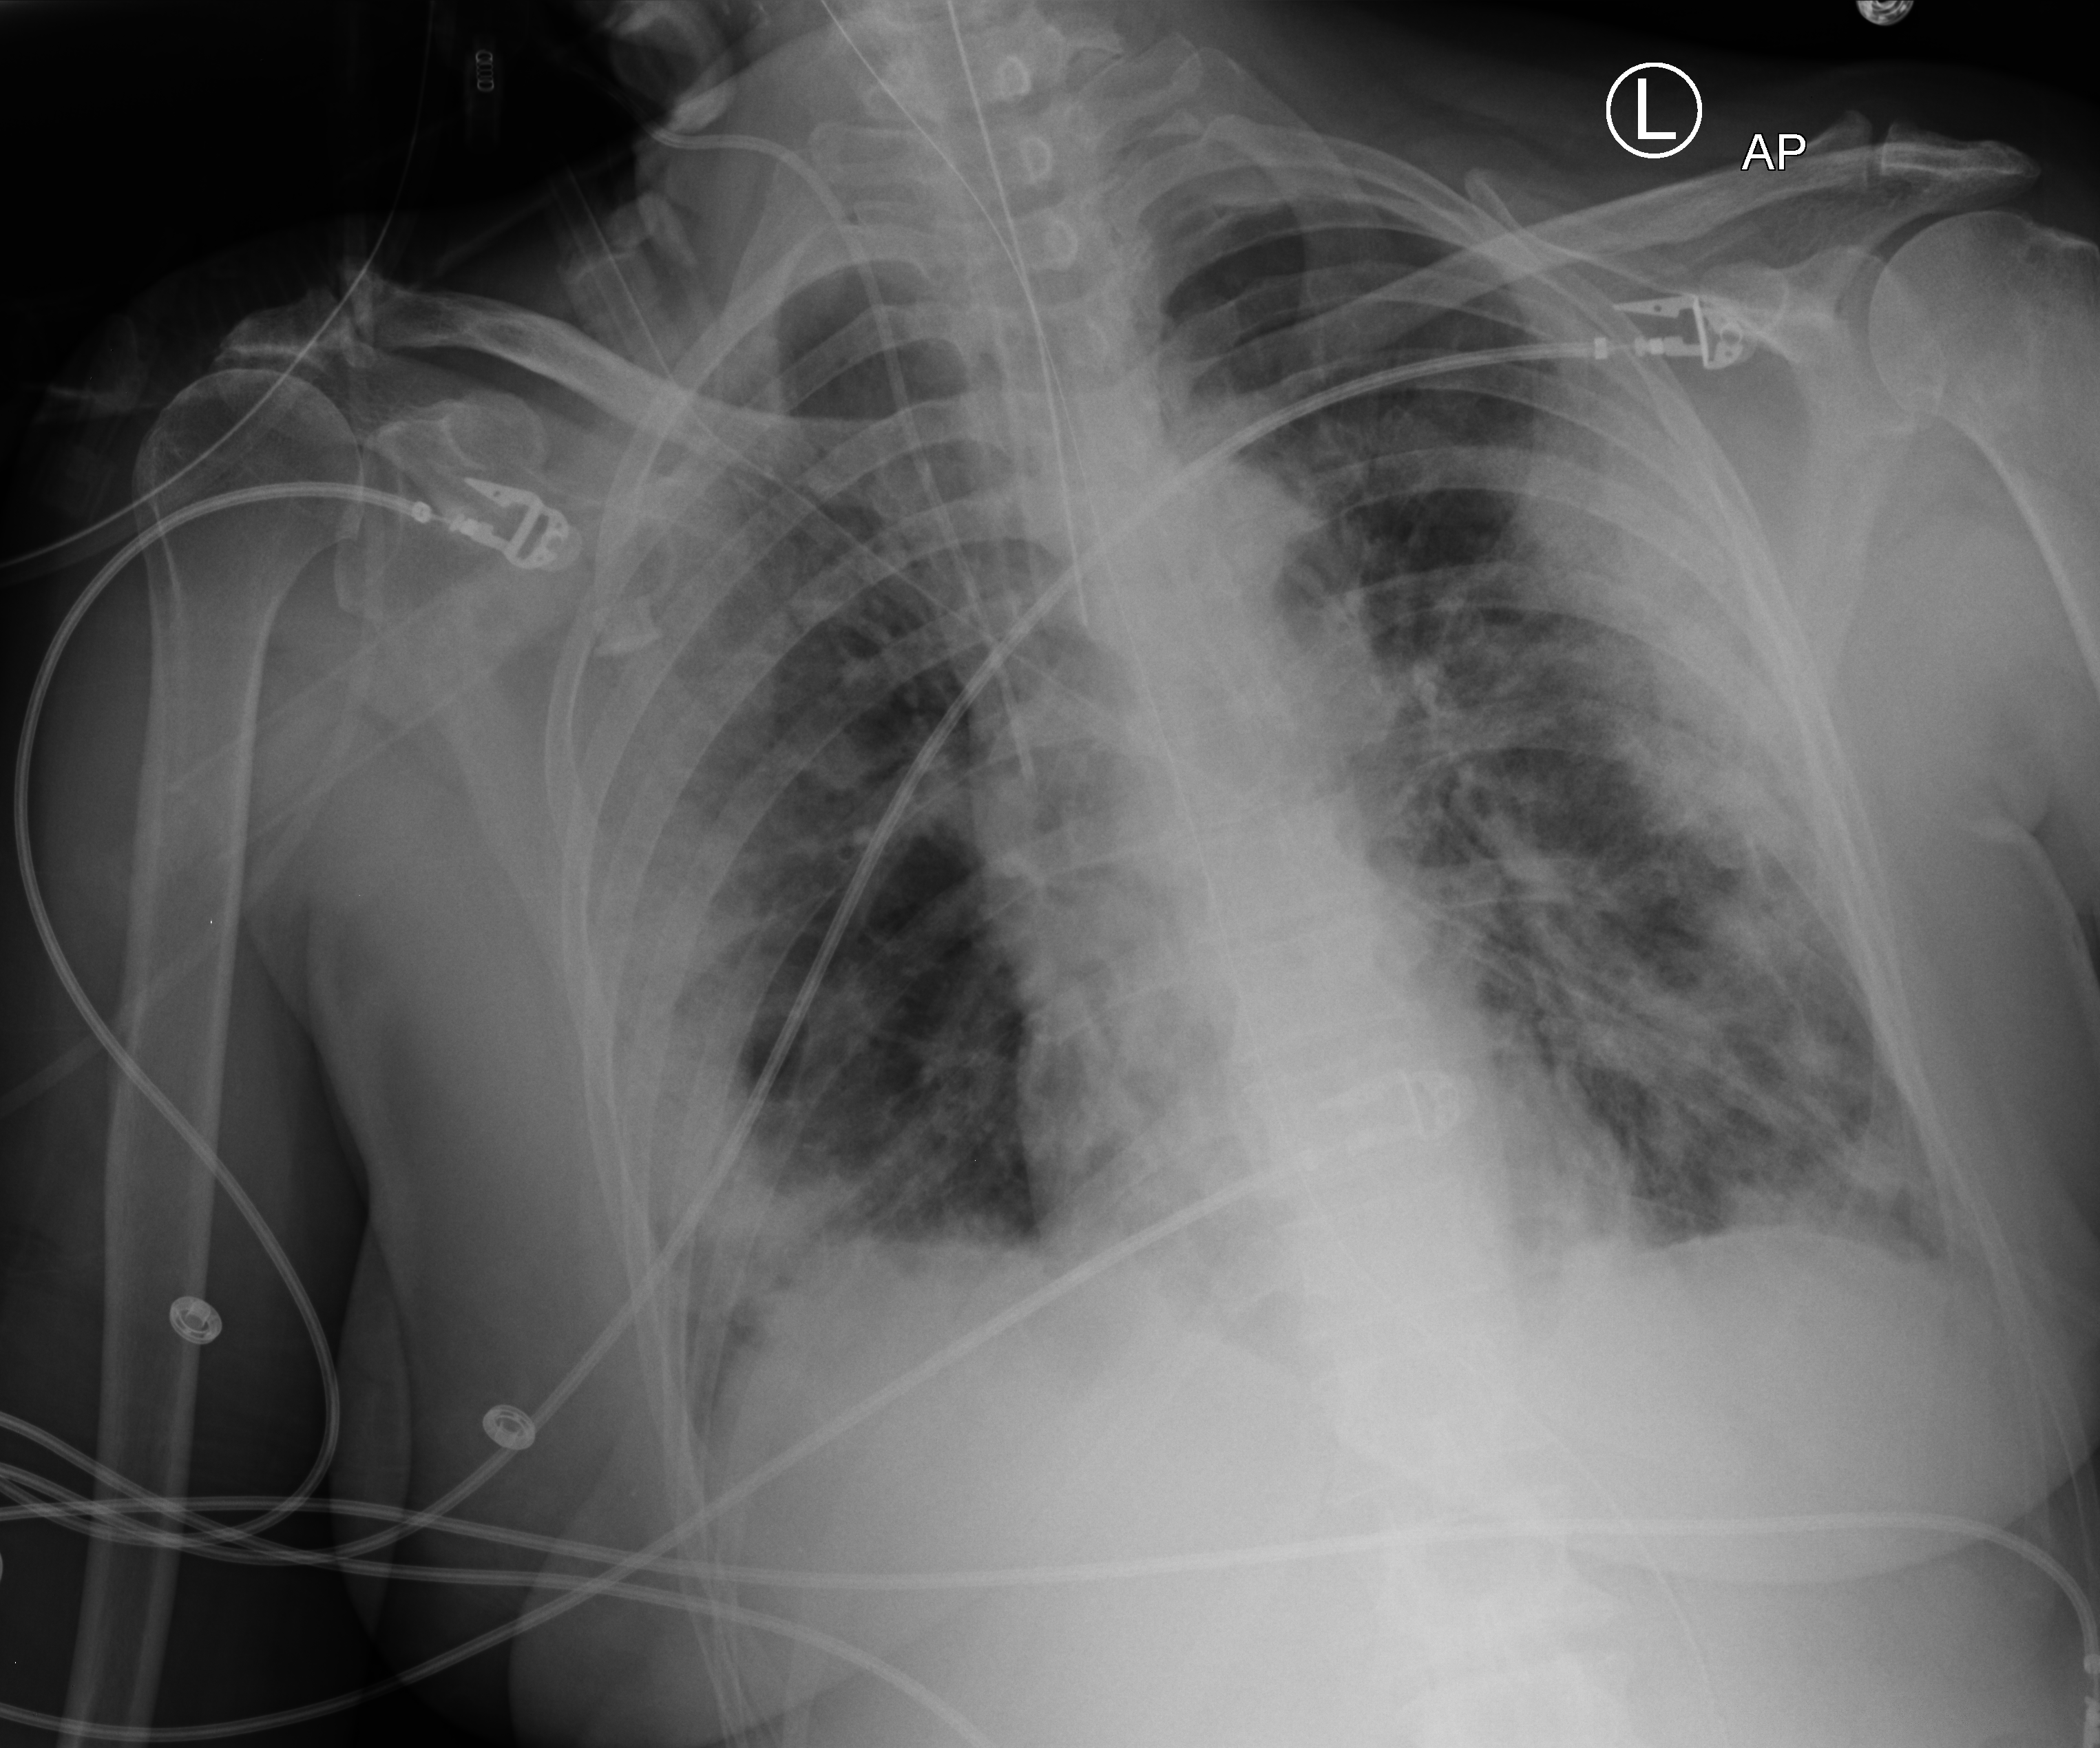
Chest X-ray (portable), anteroposterior (AP) projection. Female patient hospitalised with COVID-19, age 60–74 years.
Hospital-stay facts (about this admission, not read from this image; timing relative to this image not recorded): length of hospital stay: 18 days.